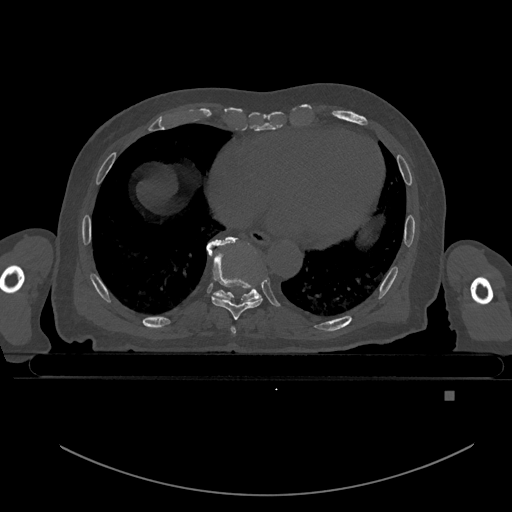
CT including the spine, one axial slice; slice 185 of 969 in the series (ordered by position); bone window (W 1800 / L 400 HU); 0.5 mm slice thickness; 512 × 512 image matrix, field of view 456 × 456 mm. Patient: male, 82 years. Case-level facts recorded for this patient, not image findings: primary cancer: prostate; vertebrae with lytic lesions (as recorded): T11, T9, T8, T2.
Annotated regions visible in this slice (semi-automatically segmented with operator editing):
- T7 vertebra: bounding box [x1, y1, x2, y2] px = [231, 326, 236, 334]
- T8 vertebra: [210, 241, 263, 320]
- T9 vertebra: [206, 236, 261, 302]